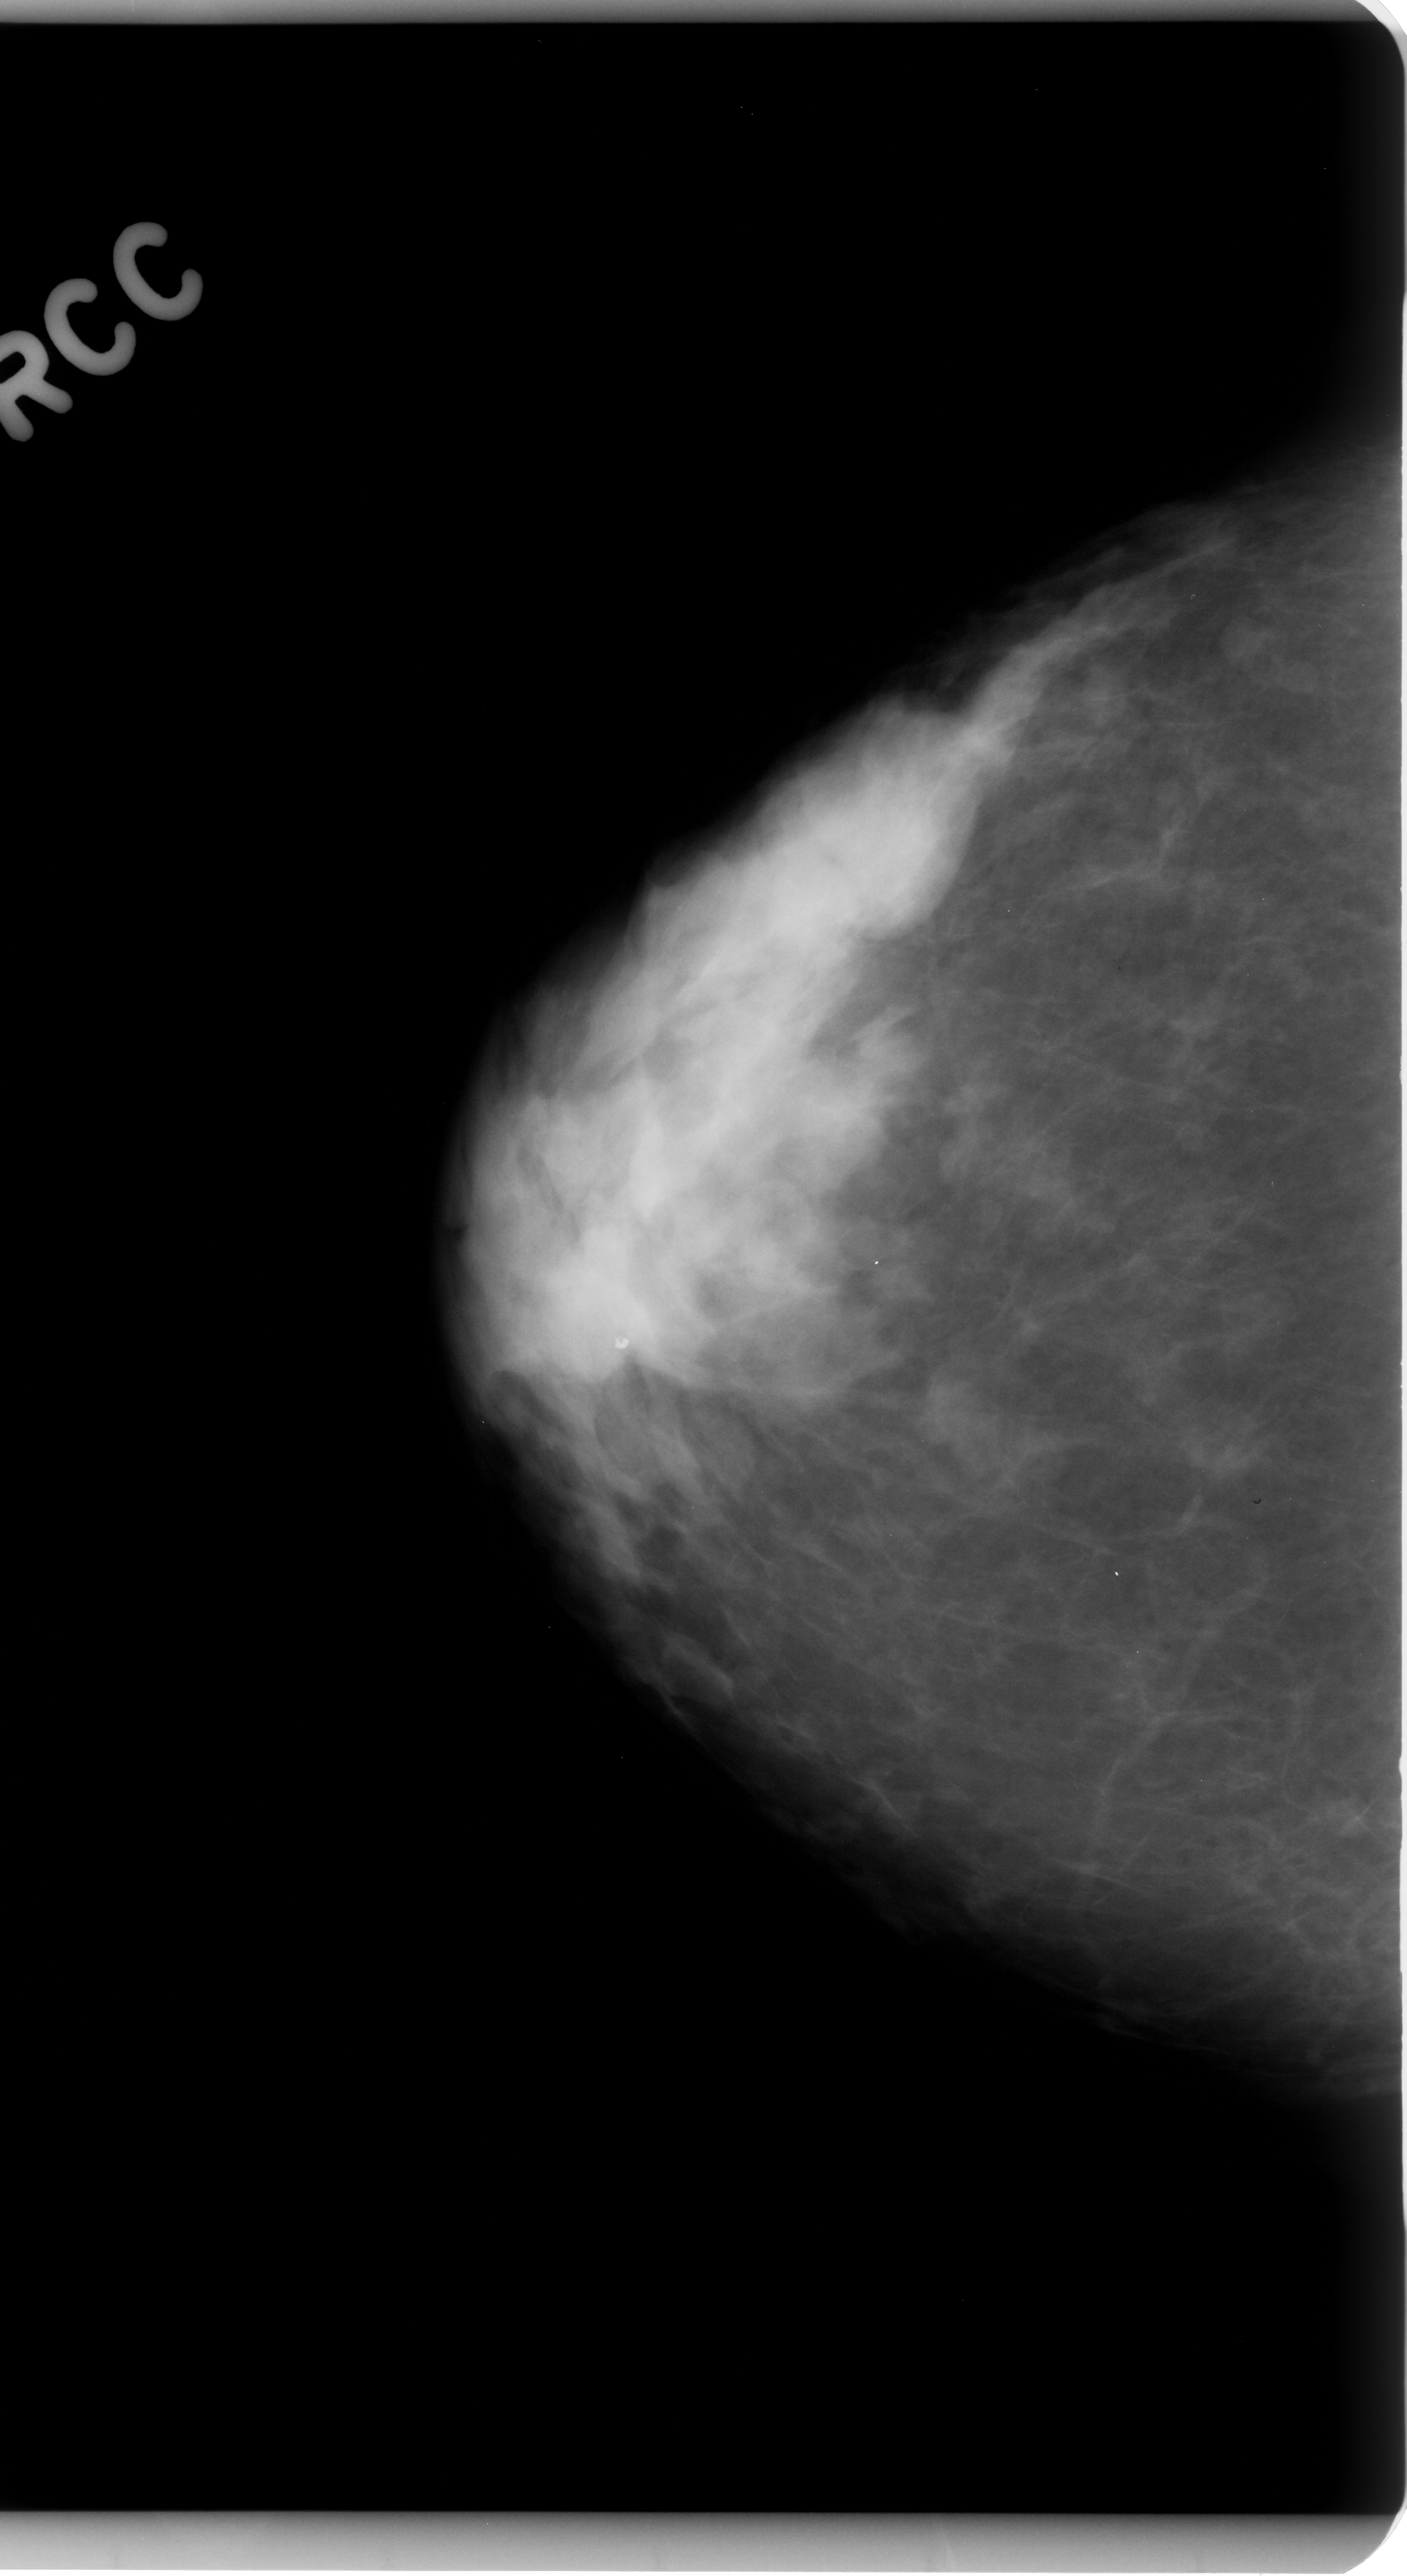
Scanned film-screen mammogram, right breast, CC view, breast composition: heterogeneously dense (BI-RADS density category 3 of 4).
Abnormality record for this image: mass, shape lobulated, margins ill defined; BI-RADS assessment category 3; pathology result (as recorded, not read from the image): benign.